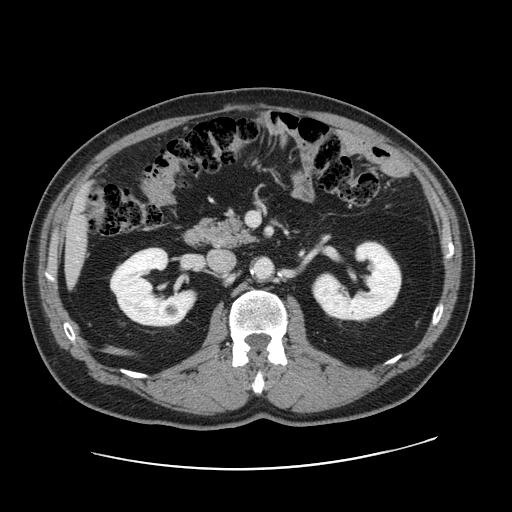
Contrast-enhanced abdominal CT, one axial slice; slice 69 of 178 in the series (ordered by position); 120 kVp; intravenous contrast given; soft-tissue window (W 400 / L 40 HU); 2.5 mm slice thickness; 512 × 512 image matrix, field of view 403 × 403 mm. Male patient, age 63 years. Case-level facts recorded for this patient, not image findings: diagnosis: colorectal cancer liver metastases, imaged before liver resection; multiple liver metastases: yes; largest metastasis: 8 cm; disease in both lobes: yes.
Structures marked on this image (expert manual segmentation):
- liver: bounding box [x1, y1, x2, y2] px = [67, 194, 88, 278]